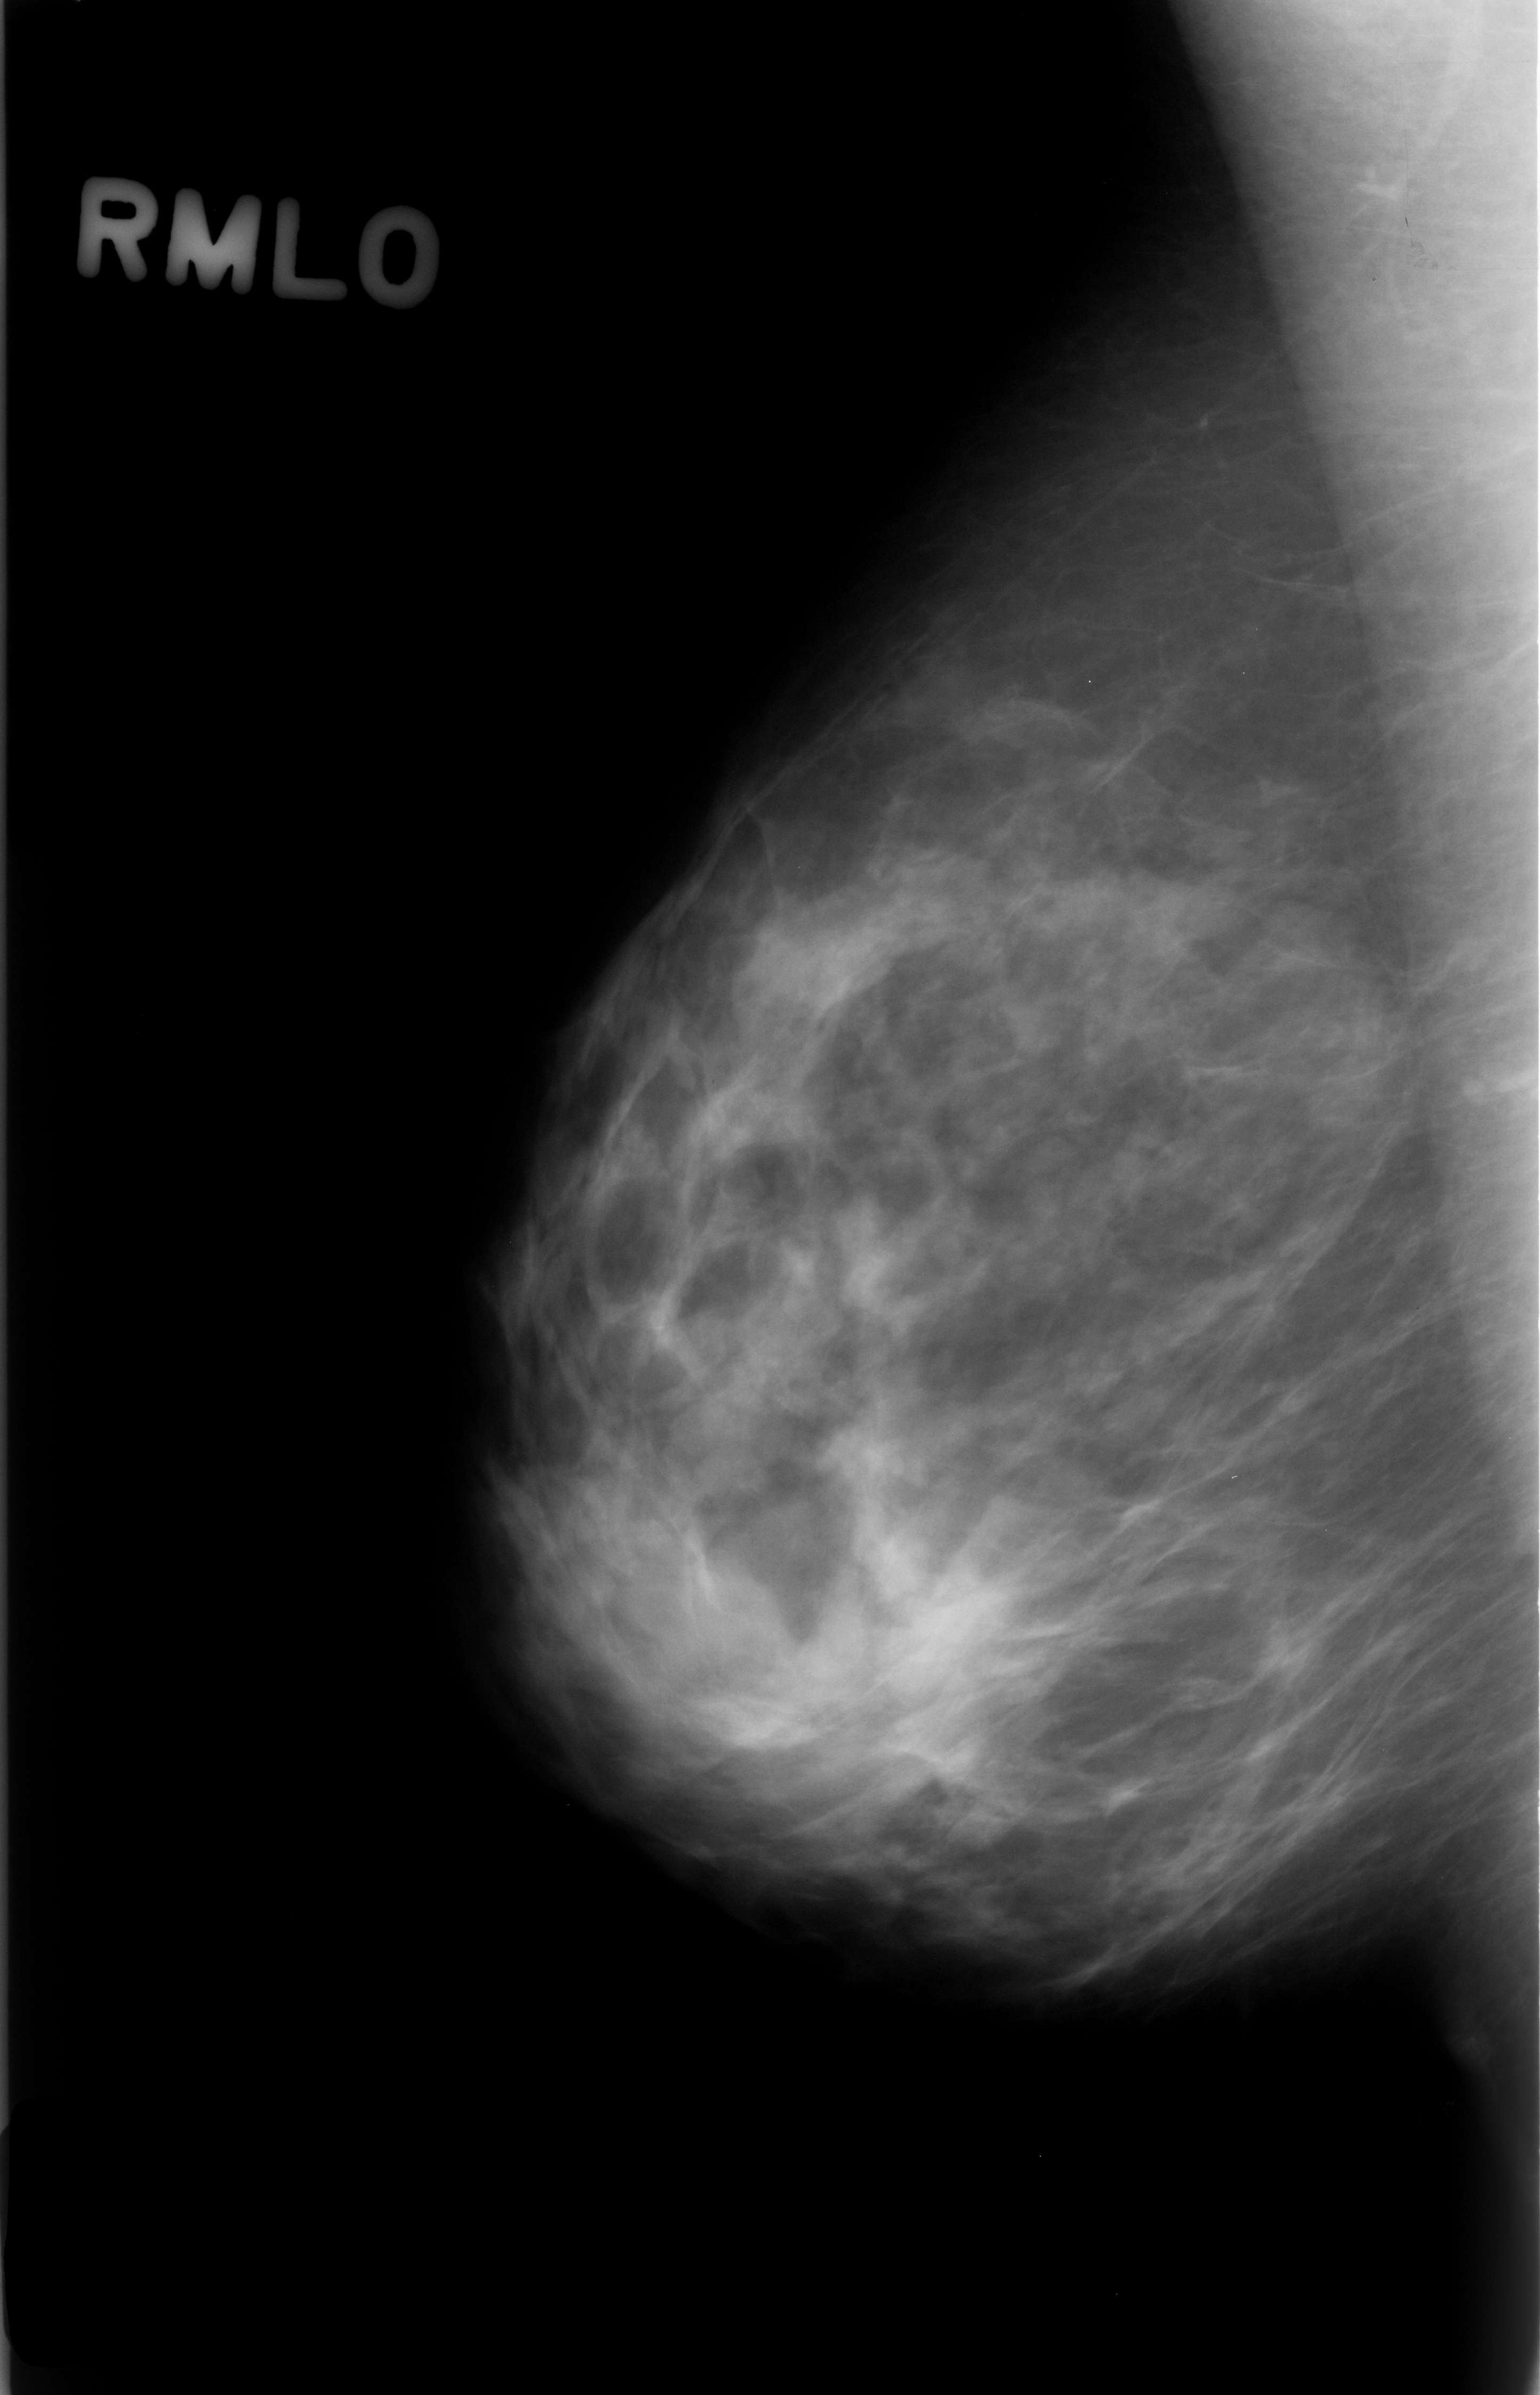
Digitized screen-film mammogram, right breast, MLO view, breast composition: scattered fibroglandular densities (BI-RADS density category 2 of 4).
Marked findings (only marked abnormalities are described; nothing is implied about the rest of the image): mass, shape focal asymmetric density; BI-RADS assessment category 3; subtlety rating 5 on a 1 (subtle) to 5 (obvious) scale; benign without callback (not worked up further).